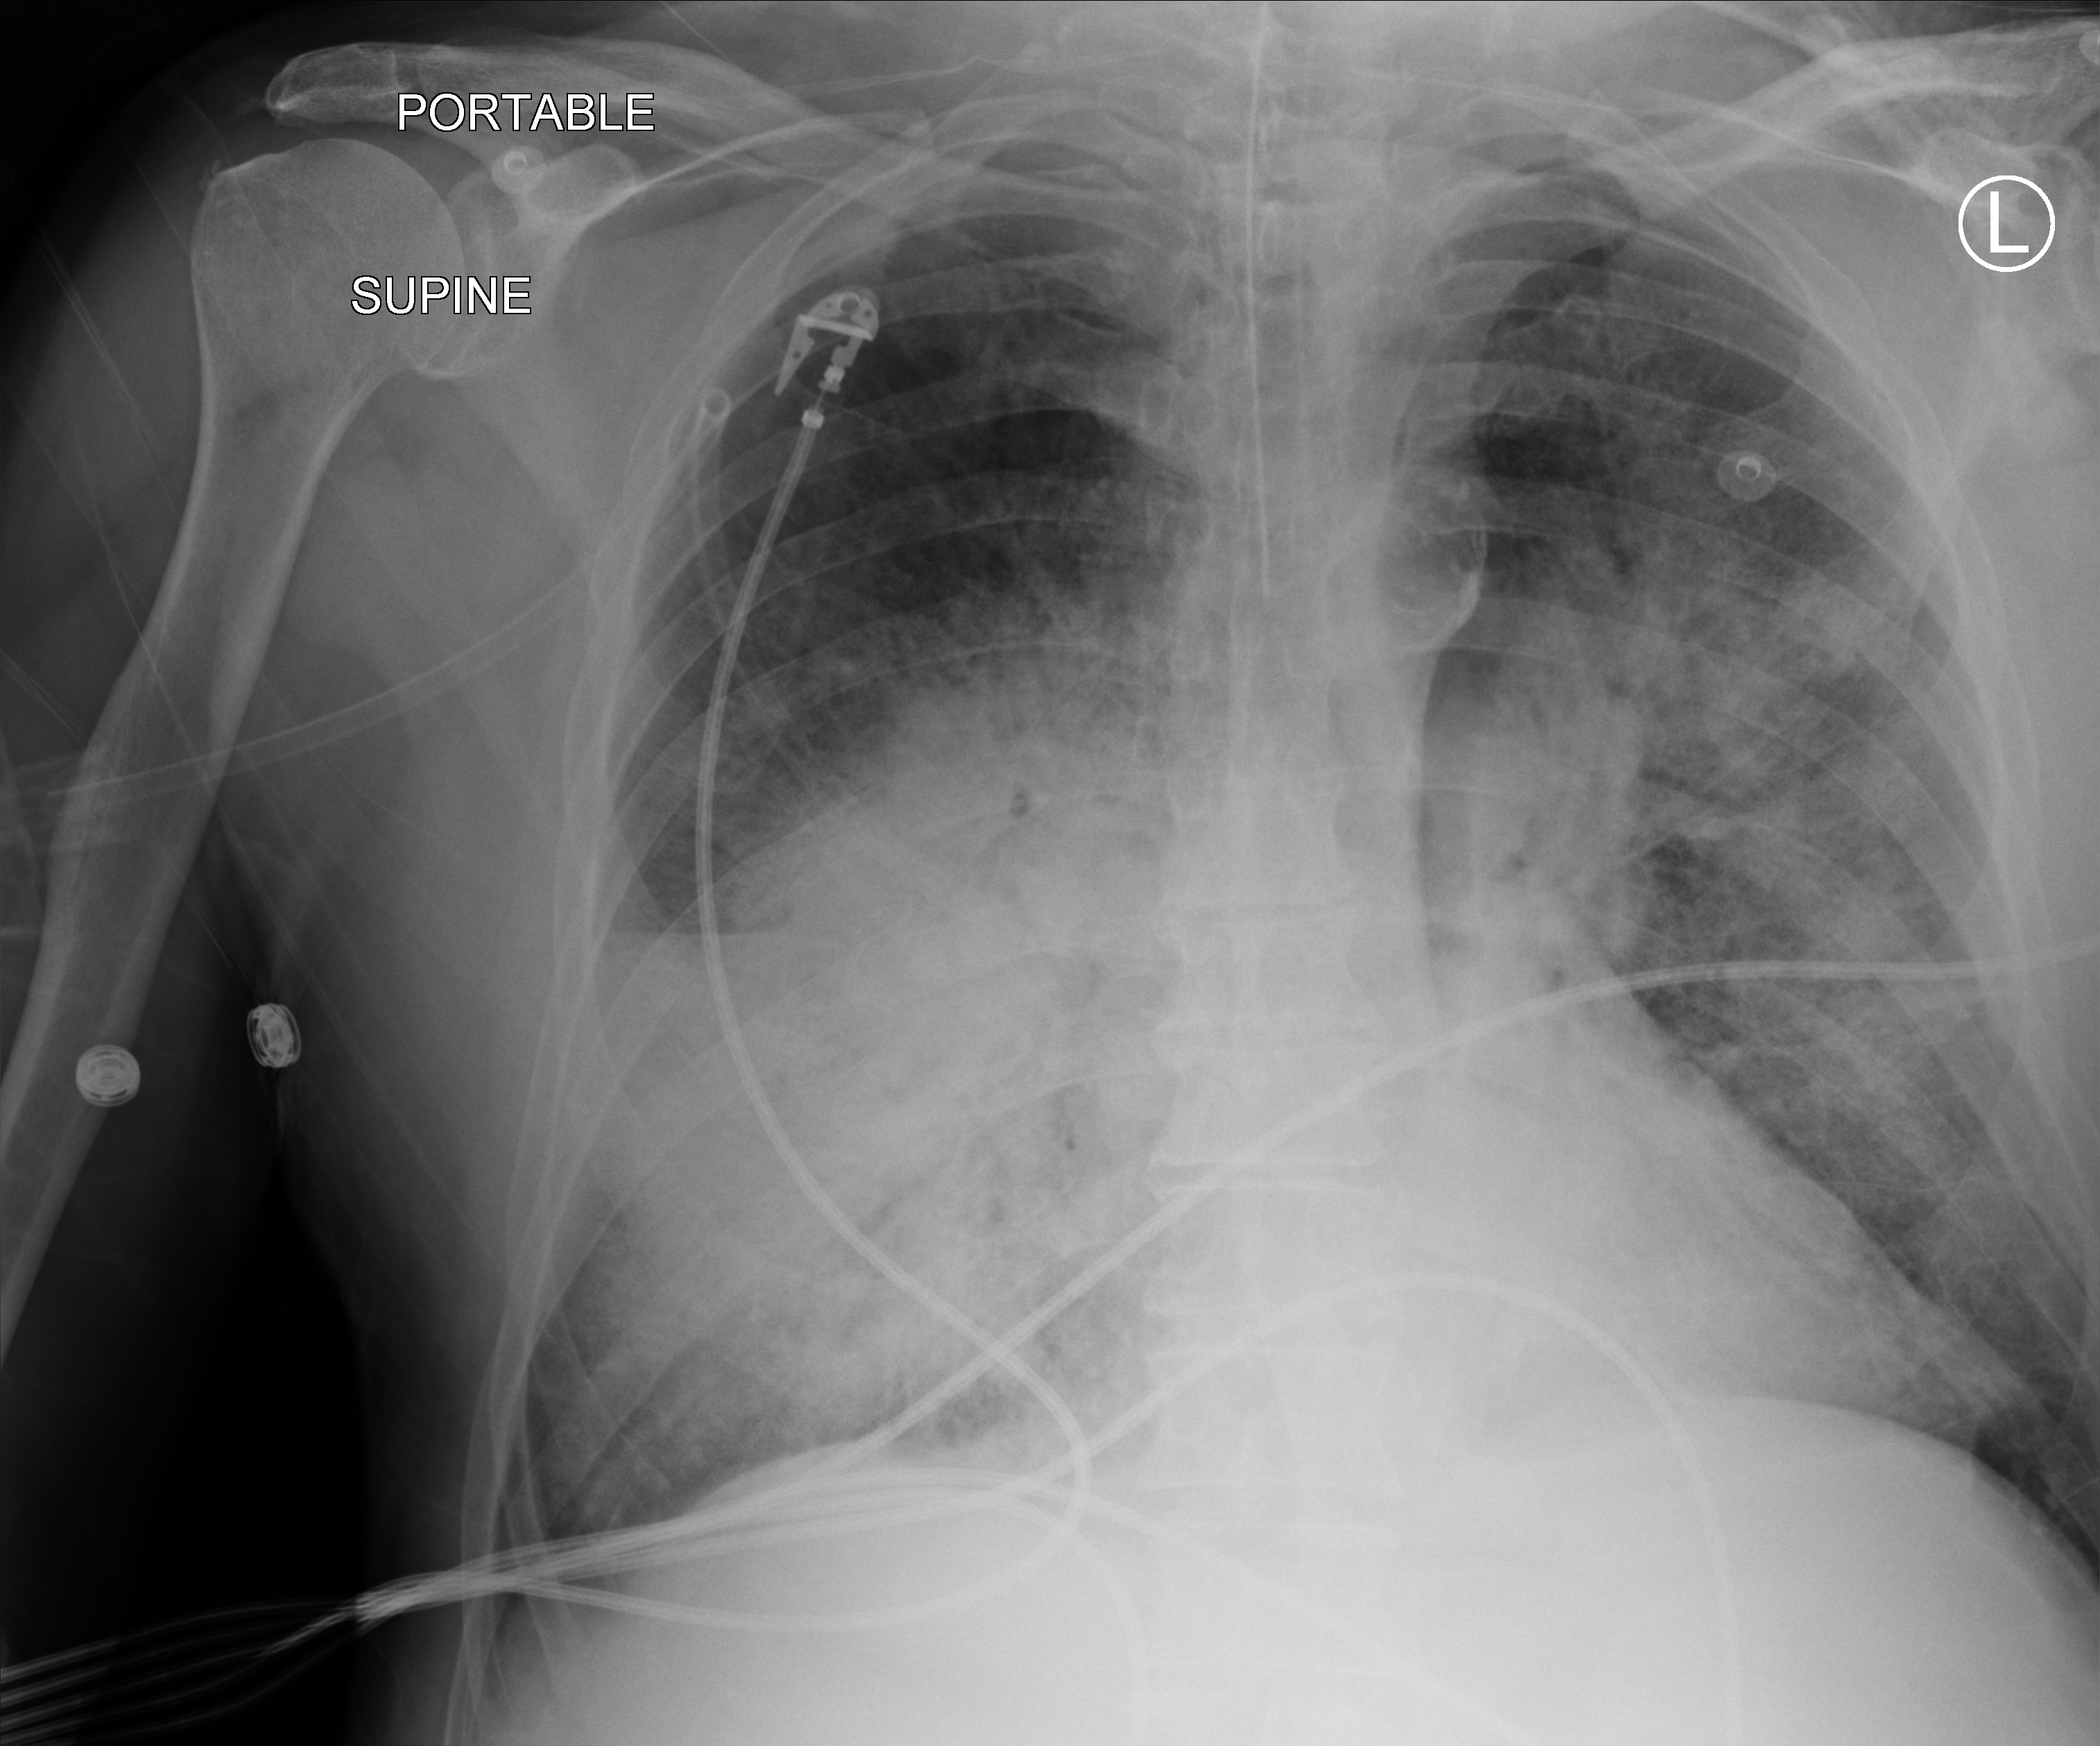
Chest X-ray (portable); anteroposterior (AP) projection. Patient hospitalised with COVID-19; male, aged 60–74 years.
Hospital-stay facts (about this admission, not read from this image; timing relative to this image not recorded):
- mechanically ventilated during this hospital stay: yes
- COPD (admission record): no